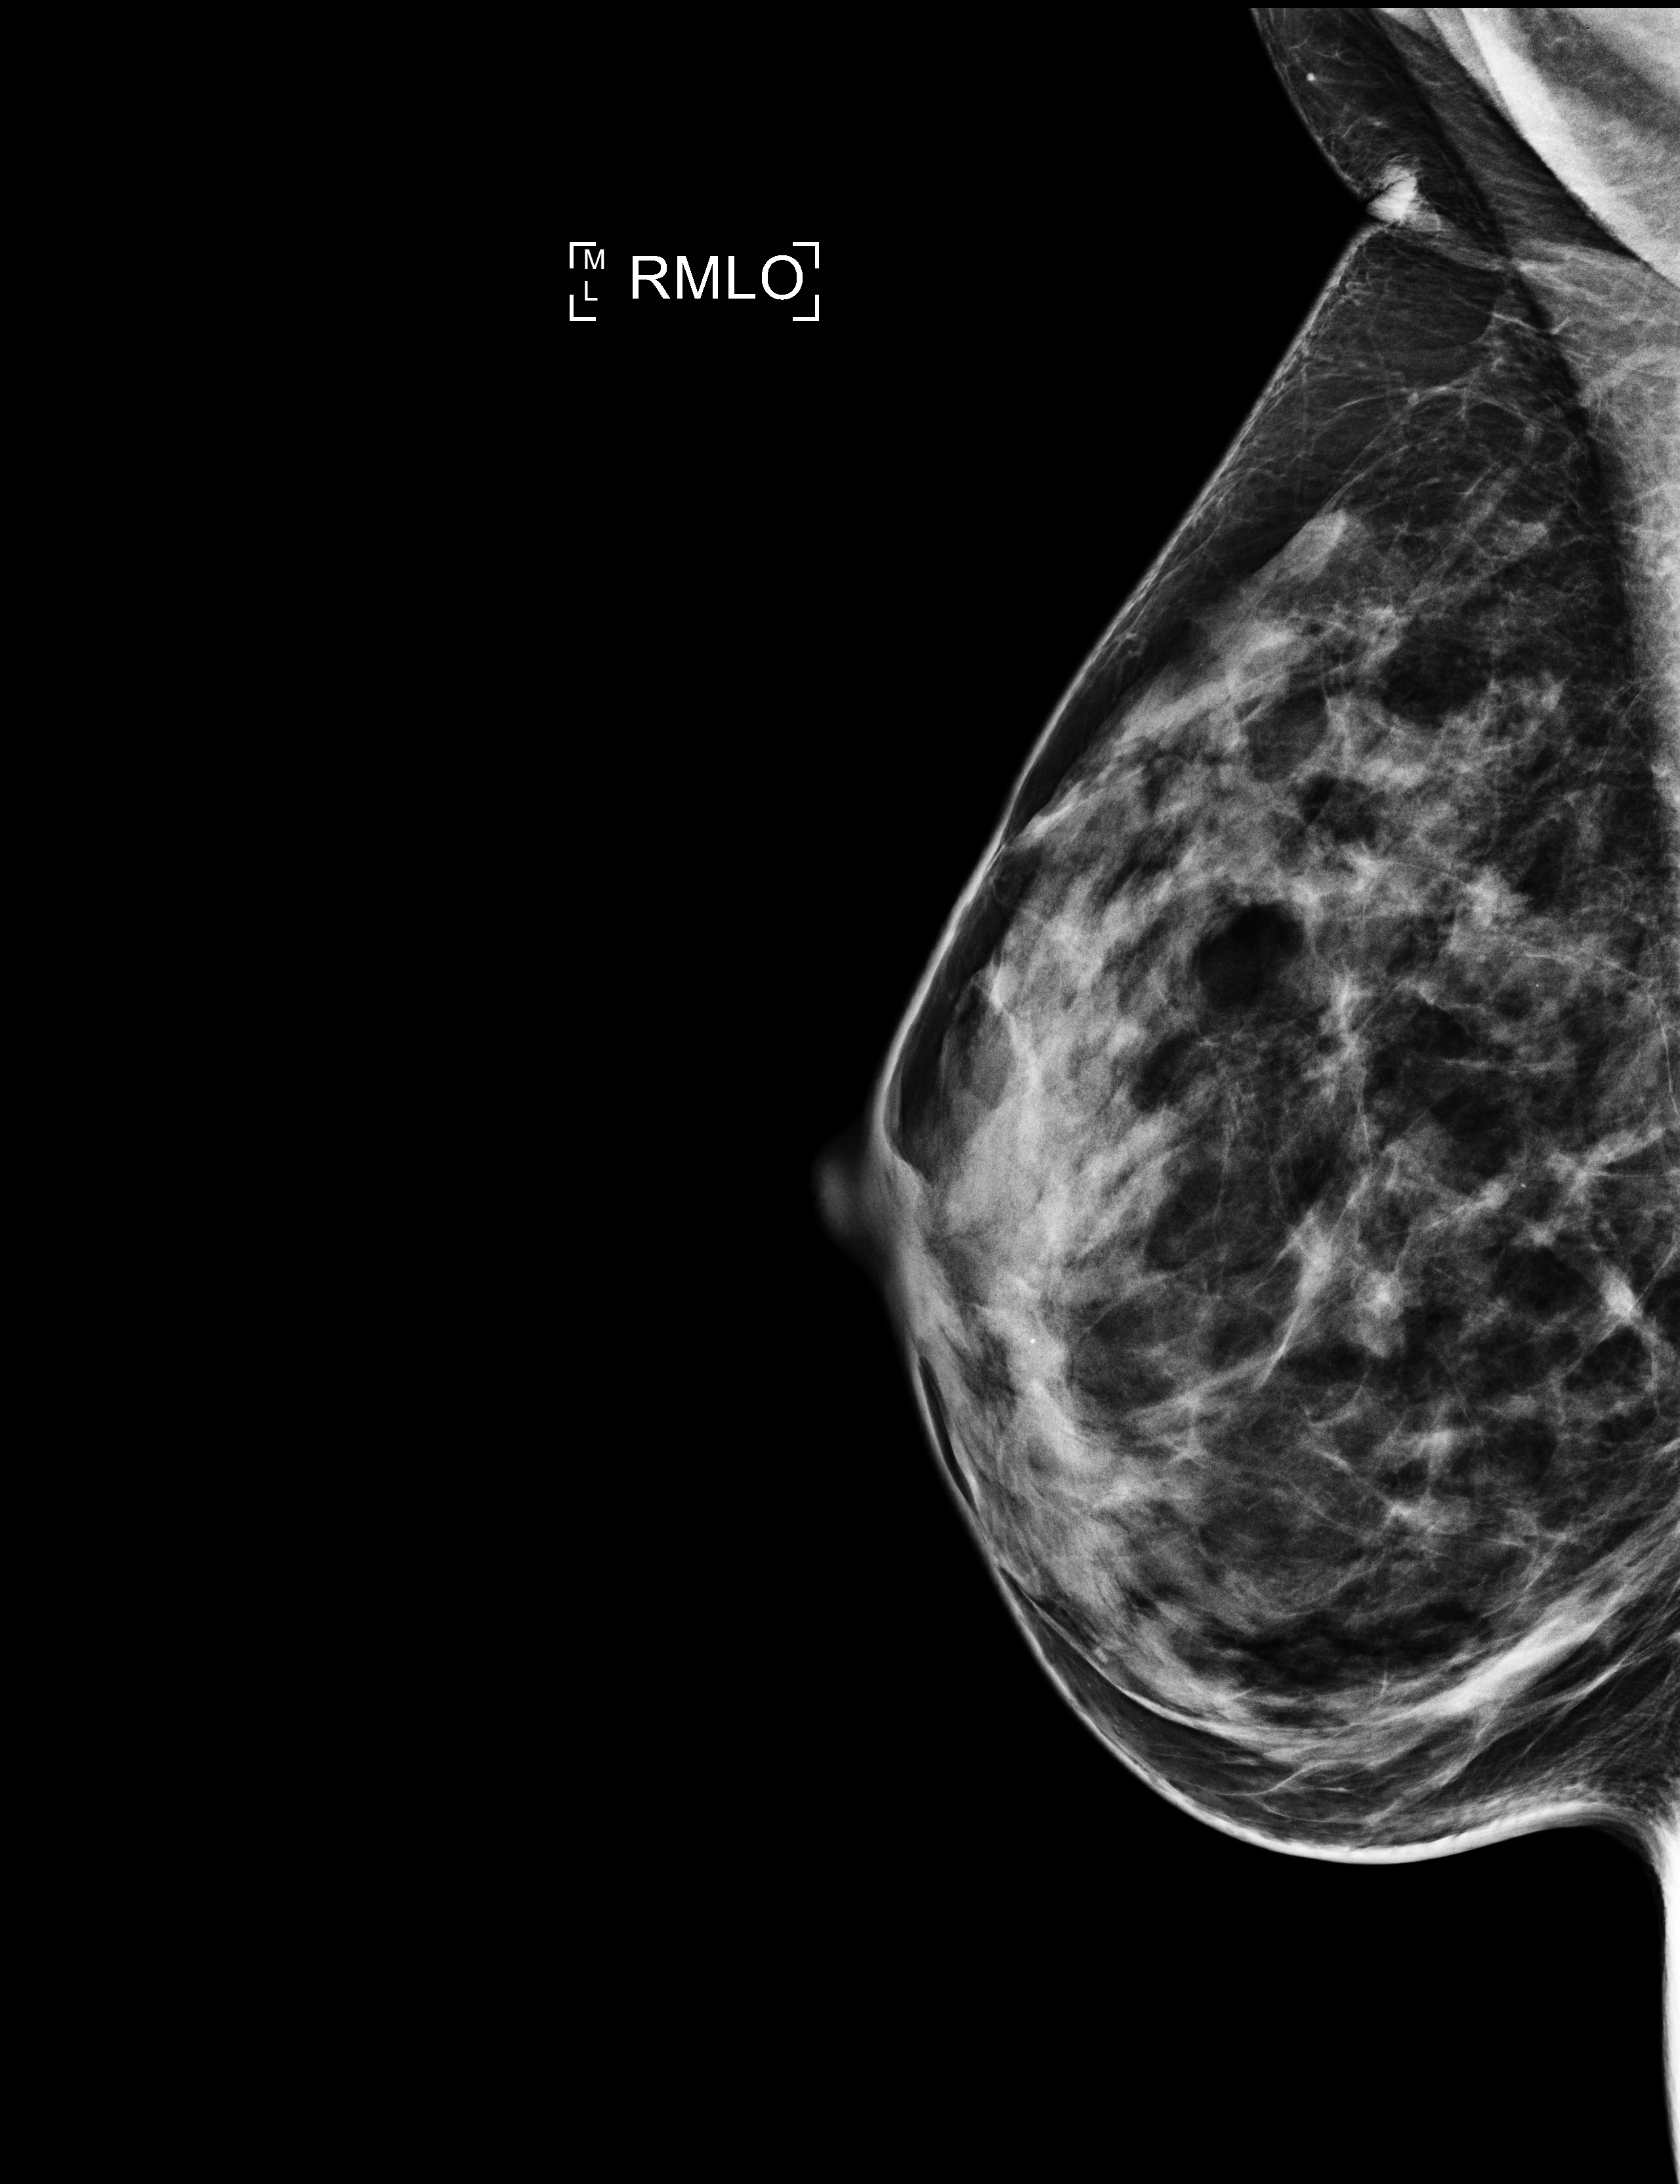
Full-field digital mammogram (FFDM); right breast; MLO view; annual screening mammography examination; compressed breast thickness 43 mm. Female patient, age 52 years.
- BI-RADS breast density category at the screening exam (both breasts, scale 1–4): 3
- final BI-RADS category for the screening round (tomosynthesis exam, both breasts): category 2
- recall: no recall after this screen